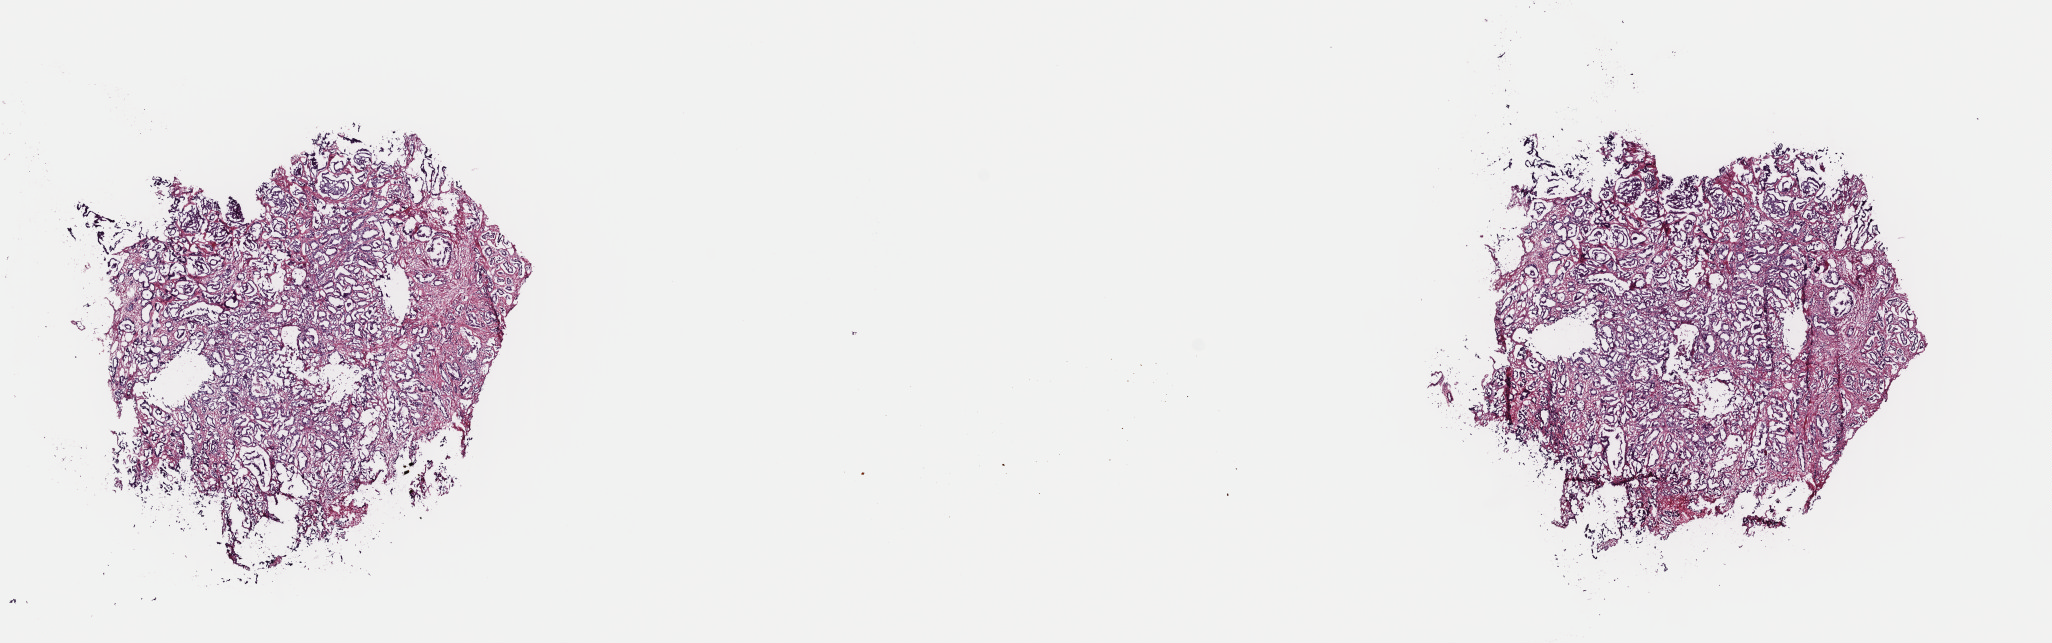
H&E whole-slide image, low-resolution overview of the scanned area, about 16.2 x 5.1 mm, frozen section from the top of the tissue portion, prostate, primary tumour sample. Patient: male, age at initial diagnosis 53 years. Gleason score: 6 (3+3). Pathologist review of this section (percent, as recorded): tumour cells 40%, tumour nuclei 80%, normal cells 0%, stromal cells 53%, necrosis 7%. Infiltration values recorded for this section: lymphocyte infiltration 2%, monocyte infiltration 0%, neutrophil infiltration 0%.
Lymph nodes positive (case pathology): 0 of 2 examined. Laterality: bilateral. Diagnosis: Adenocarcinoma, NOS (prostate gland).